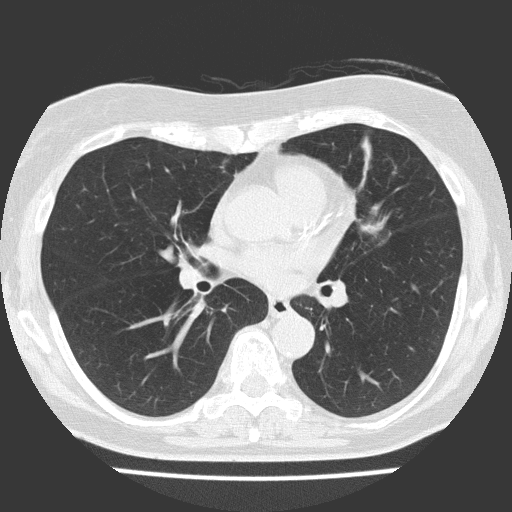
Chest CT (low-dose screening protocol), one axial image, baseline screening round, lung window (W 1500 / L -600 HU), 2 mm slice thickness, slice 75 of 151 in the series. Female, age 70 years at enrolment. Current smoker at enrolment.
- Expert-annotated lung lesion, bounding box (x1, y1, x2, y2) in pixels: (319, 175, 432, 272).
- The screening reader recorded 2 non-calcified nodules or masses ≥4 mm on this exam (left upper lobe, right upper lobe); which of them this box marks is not recorded.
- Participant outcome: lung cancer diagnosed 25 days after this screen — adenocarcinoma, NOS, left upper lobe, poorly differentiated (G3), stage IV (AJCC 6th edition), 30 mm at pathology.